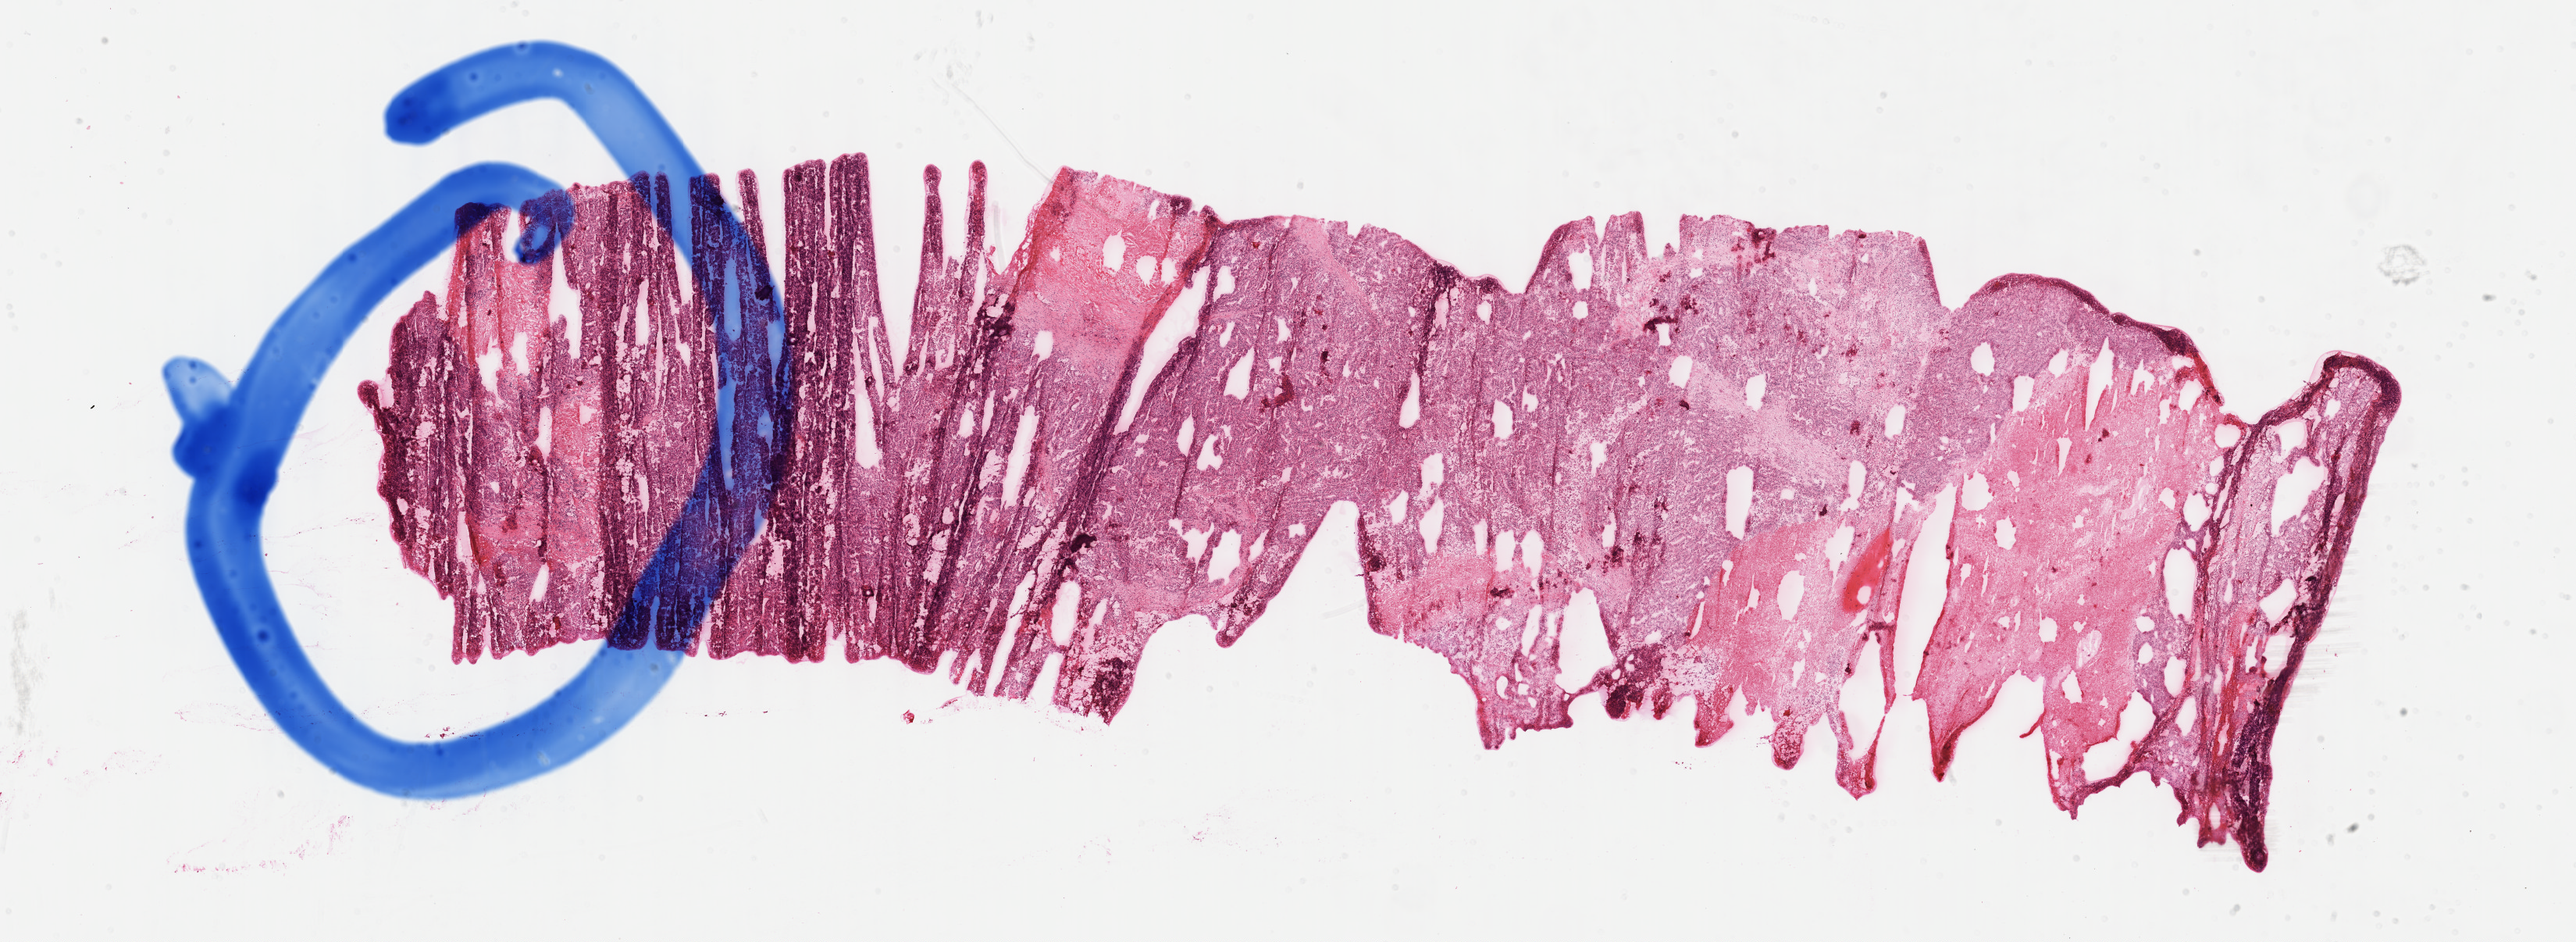
Whole-slide histology image, H&E-stained, shown as a low-resolution overview of the whole scanned area (about 26.7 x 9.8 mm, acquisition: 40x scan); formalin-fixed paraffin-embedded (FFPE) diagnostic section; kidney, primary tumour sample. Female, age 44 years at initial diagnosis. Histologic grade: G3 (poorly differentiated).
Histologic diagnosis: Clear cell adenocarcinoma, NOS. AJCC pathologic stage: IV.